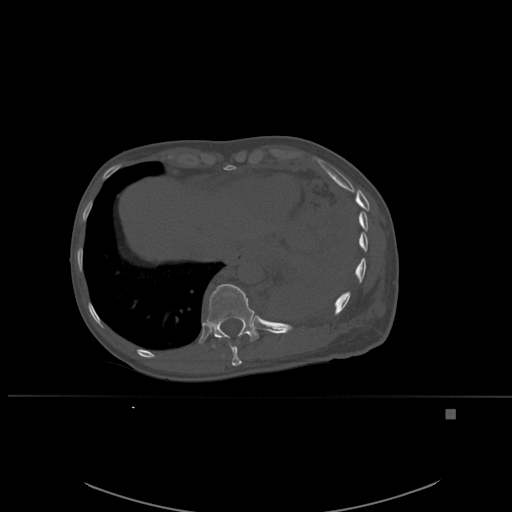
CT including the spine, one axial slice. Bone window (W 1800 / L 400 HU). 1.5 mm slice thickness. 512 × 512 image matrix, field of view 440 × 440 mm. Female patient, age 45 years. Case-level facts recorded for this patient, not image findings: primary cancer: lung.
Outlined on this slice (semi-automatically segmented with operator editing):
- T10 vertebra: bounding box <217,337,242,366> (left, top, right, bottom; pixels)
- T11 vertebra: <206,284,259,348>